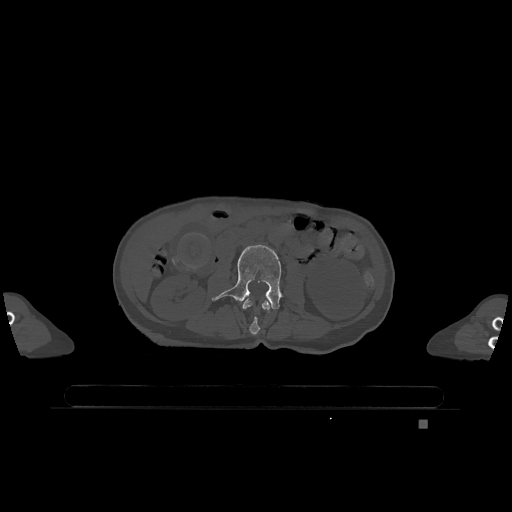
CT including the spine, one axial slice. Position 371 of 1317 along the scan axis. Bone window (W 1800 / L 400 HU). 512 × 512 image matrix, field of view 500 × 500 mm. Patient: female, 74 years. Case-level facts recorded for this patient, not image findings: primary cancer: lung; vertebrae with lytic lesions (as recorded): T1, T4, T5, T6, L4, L5.
Outlined on this slice (semi-automatically segmented with operator editing):
- L2 vertebra: bounding box [x1, y1, x2, y2] px = [242, 298, 271, 335]
- L3 vertebra: [212, 245, 282, 310]